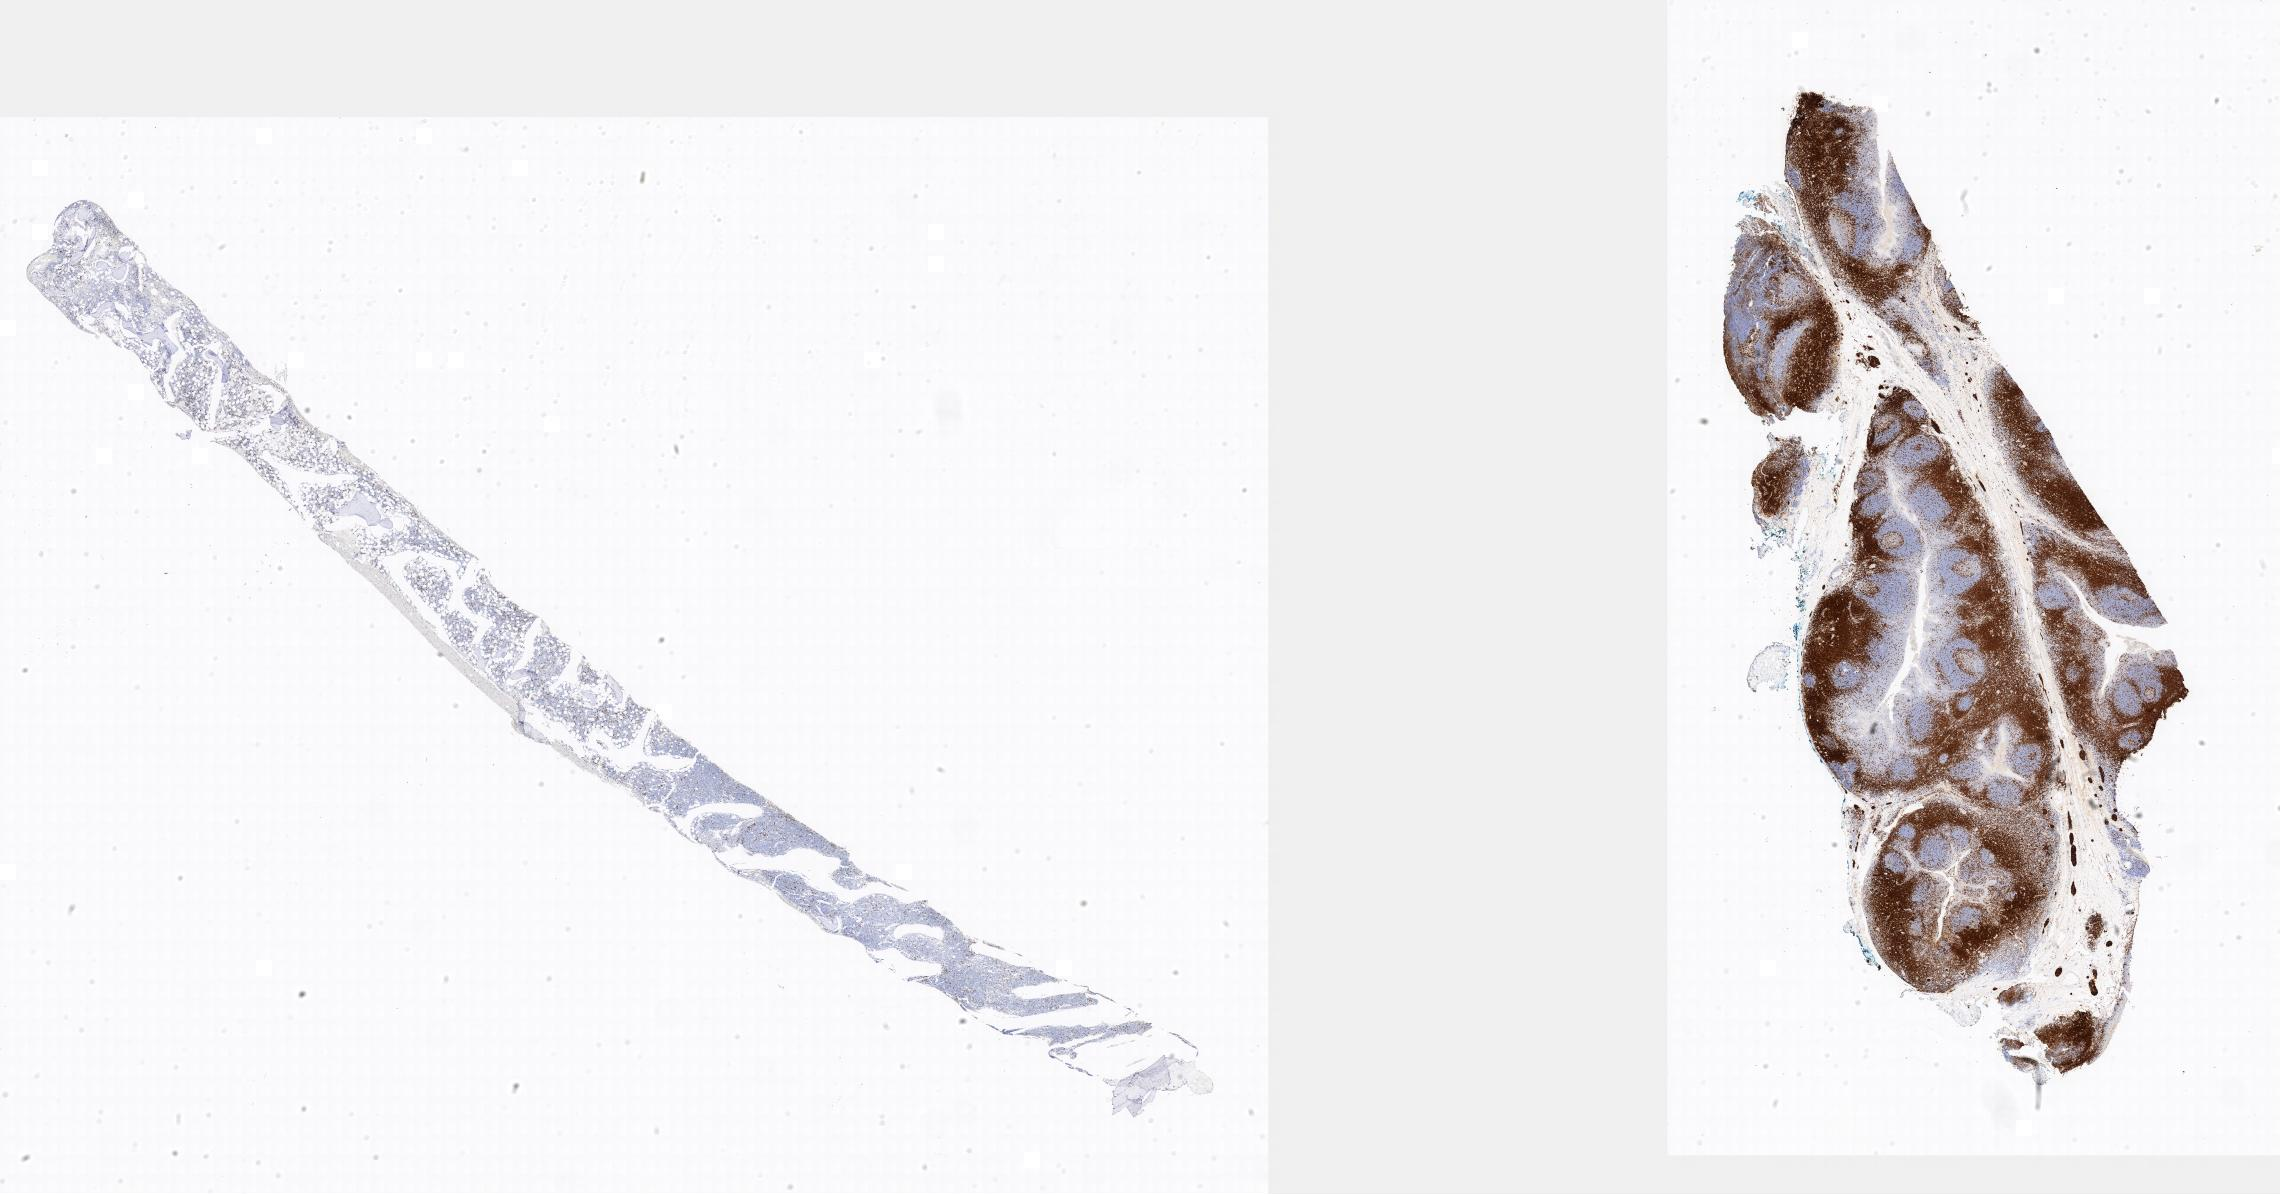
Immunohistochemistry (IHC) whole-slide image stained for CD3, a low-resolution overview of the entire scanned area. Tumor tissue. Patient male; age 12 years.
Diagnosis: Burkitt lymphoma, NOS.